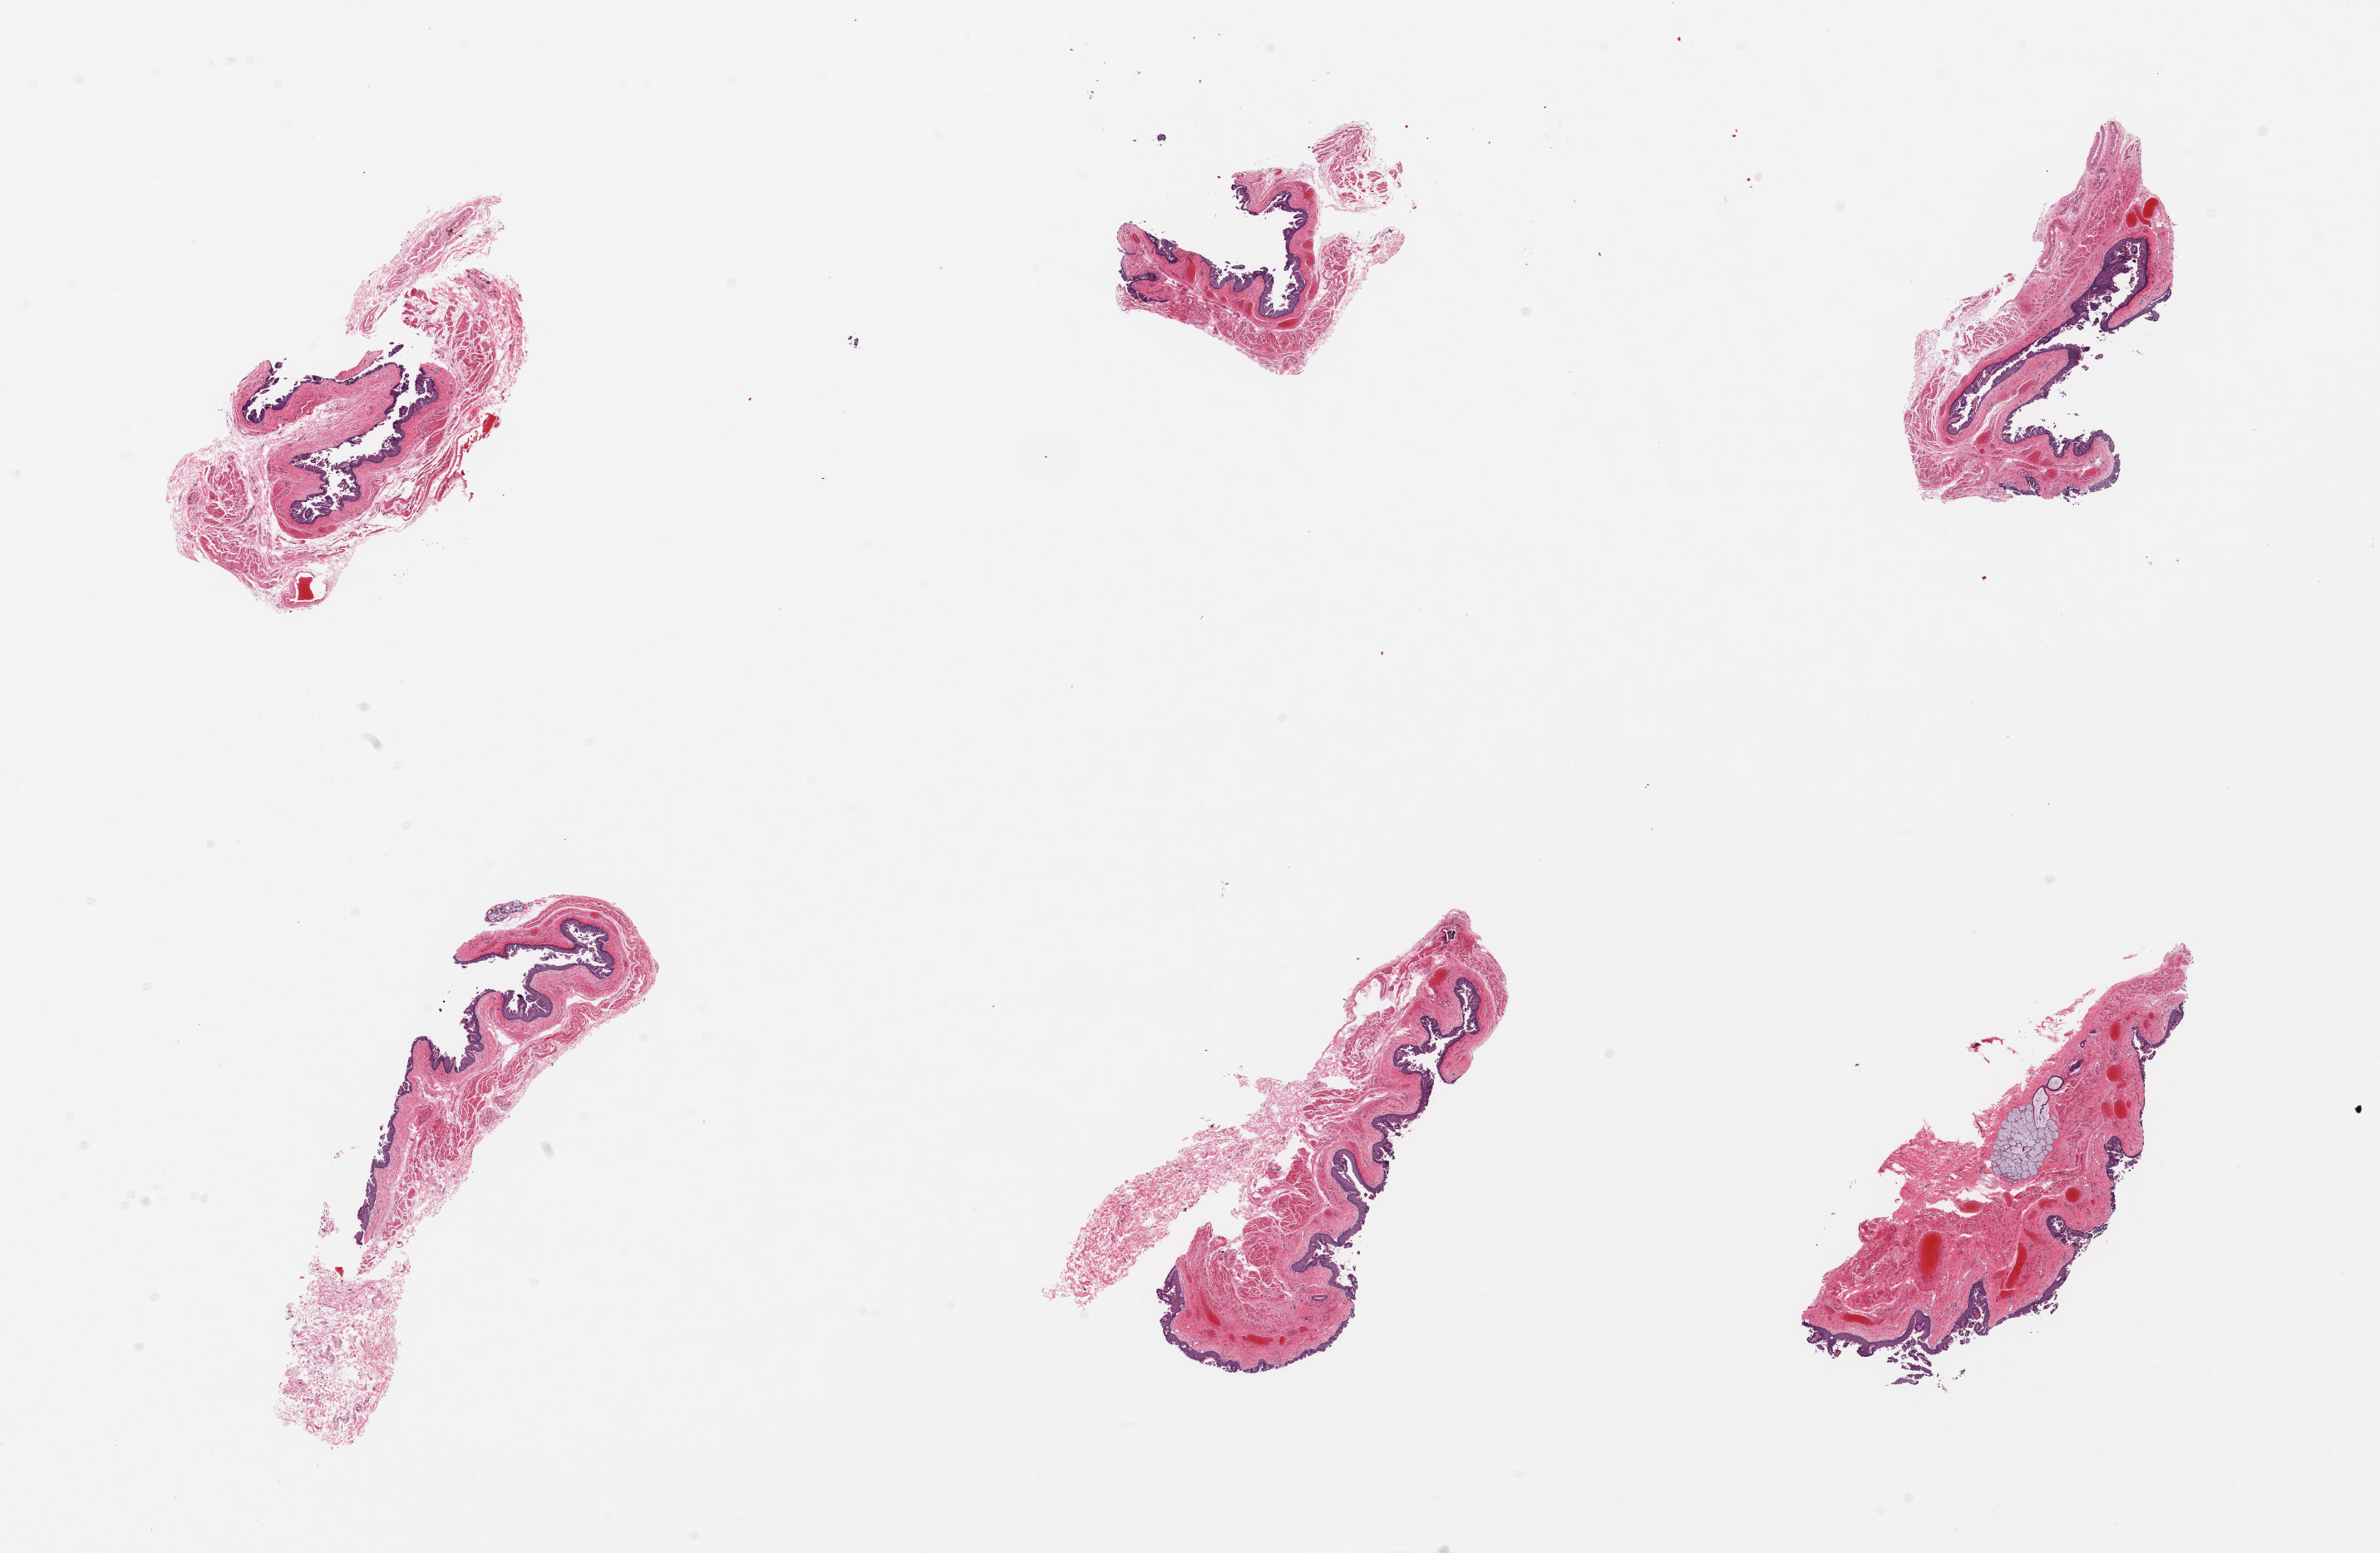
H&E whole-slide image, brightfield — a low-resolution overview of the entire scanned area, about 22.6 x 14.8 mm; PAXgene-fixed paraffin-embedded (PFPE) section; section of esophageal mucous membrane (target tissue); tissue donor sample. Female donor.
- reviewer comment on this tissue sample: 6 pieces; 60% epithelium sloughed